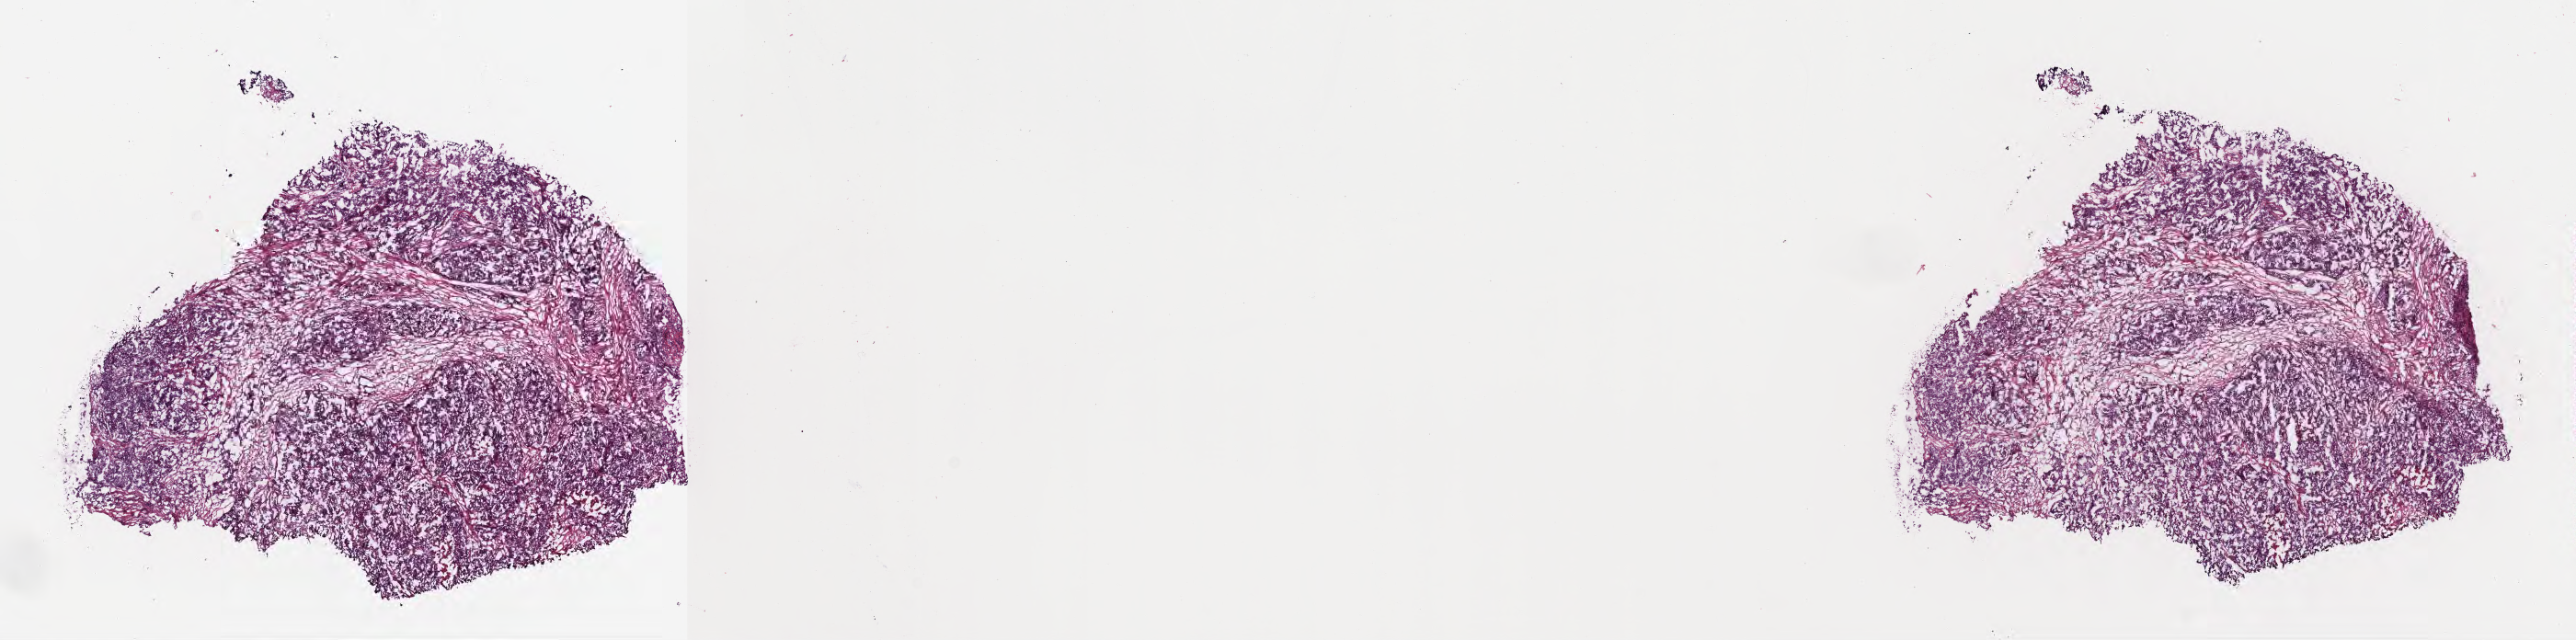
Whole-slide image, H&E stain — whole scanned area (about 22.6 x 5.6 mm) shown as a low-resolution overview. Cryosection. Specimen: metastatic tumor tissue, resected from specified parts of peritoneum. Female patient. Composition of this section per pathologist review: tumor cells 100%, tumor nuclei 90%, stromal cells 0%, necrosis 0%, normal cells 0%. Infiltration values recorded for this section: lymphocyte infiltration 0%, monocyte infiltration 0%, neutrophil infiltration 0%.
Patient diagnosis (primary): Adenocarcinoma, metastatic, NOS. Section: bottom of the tissue portion.